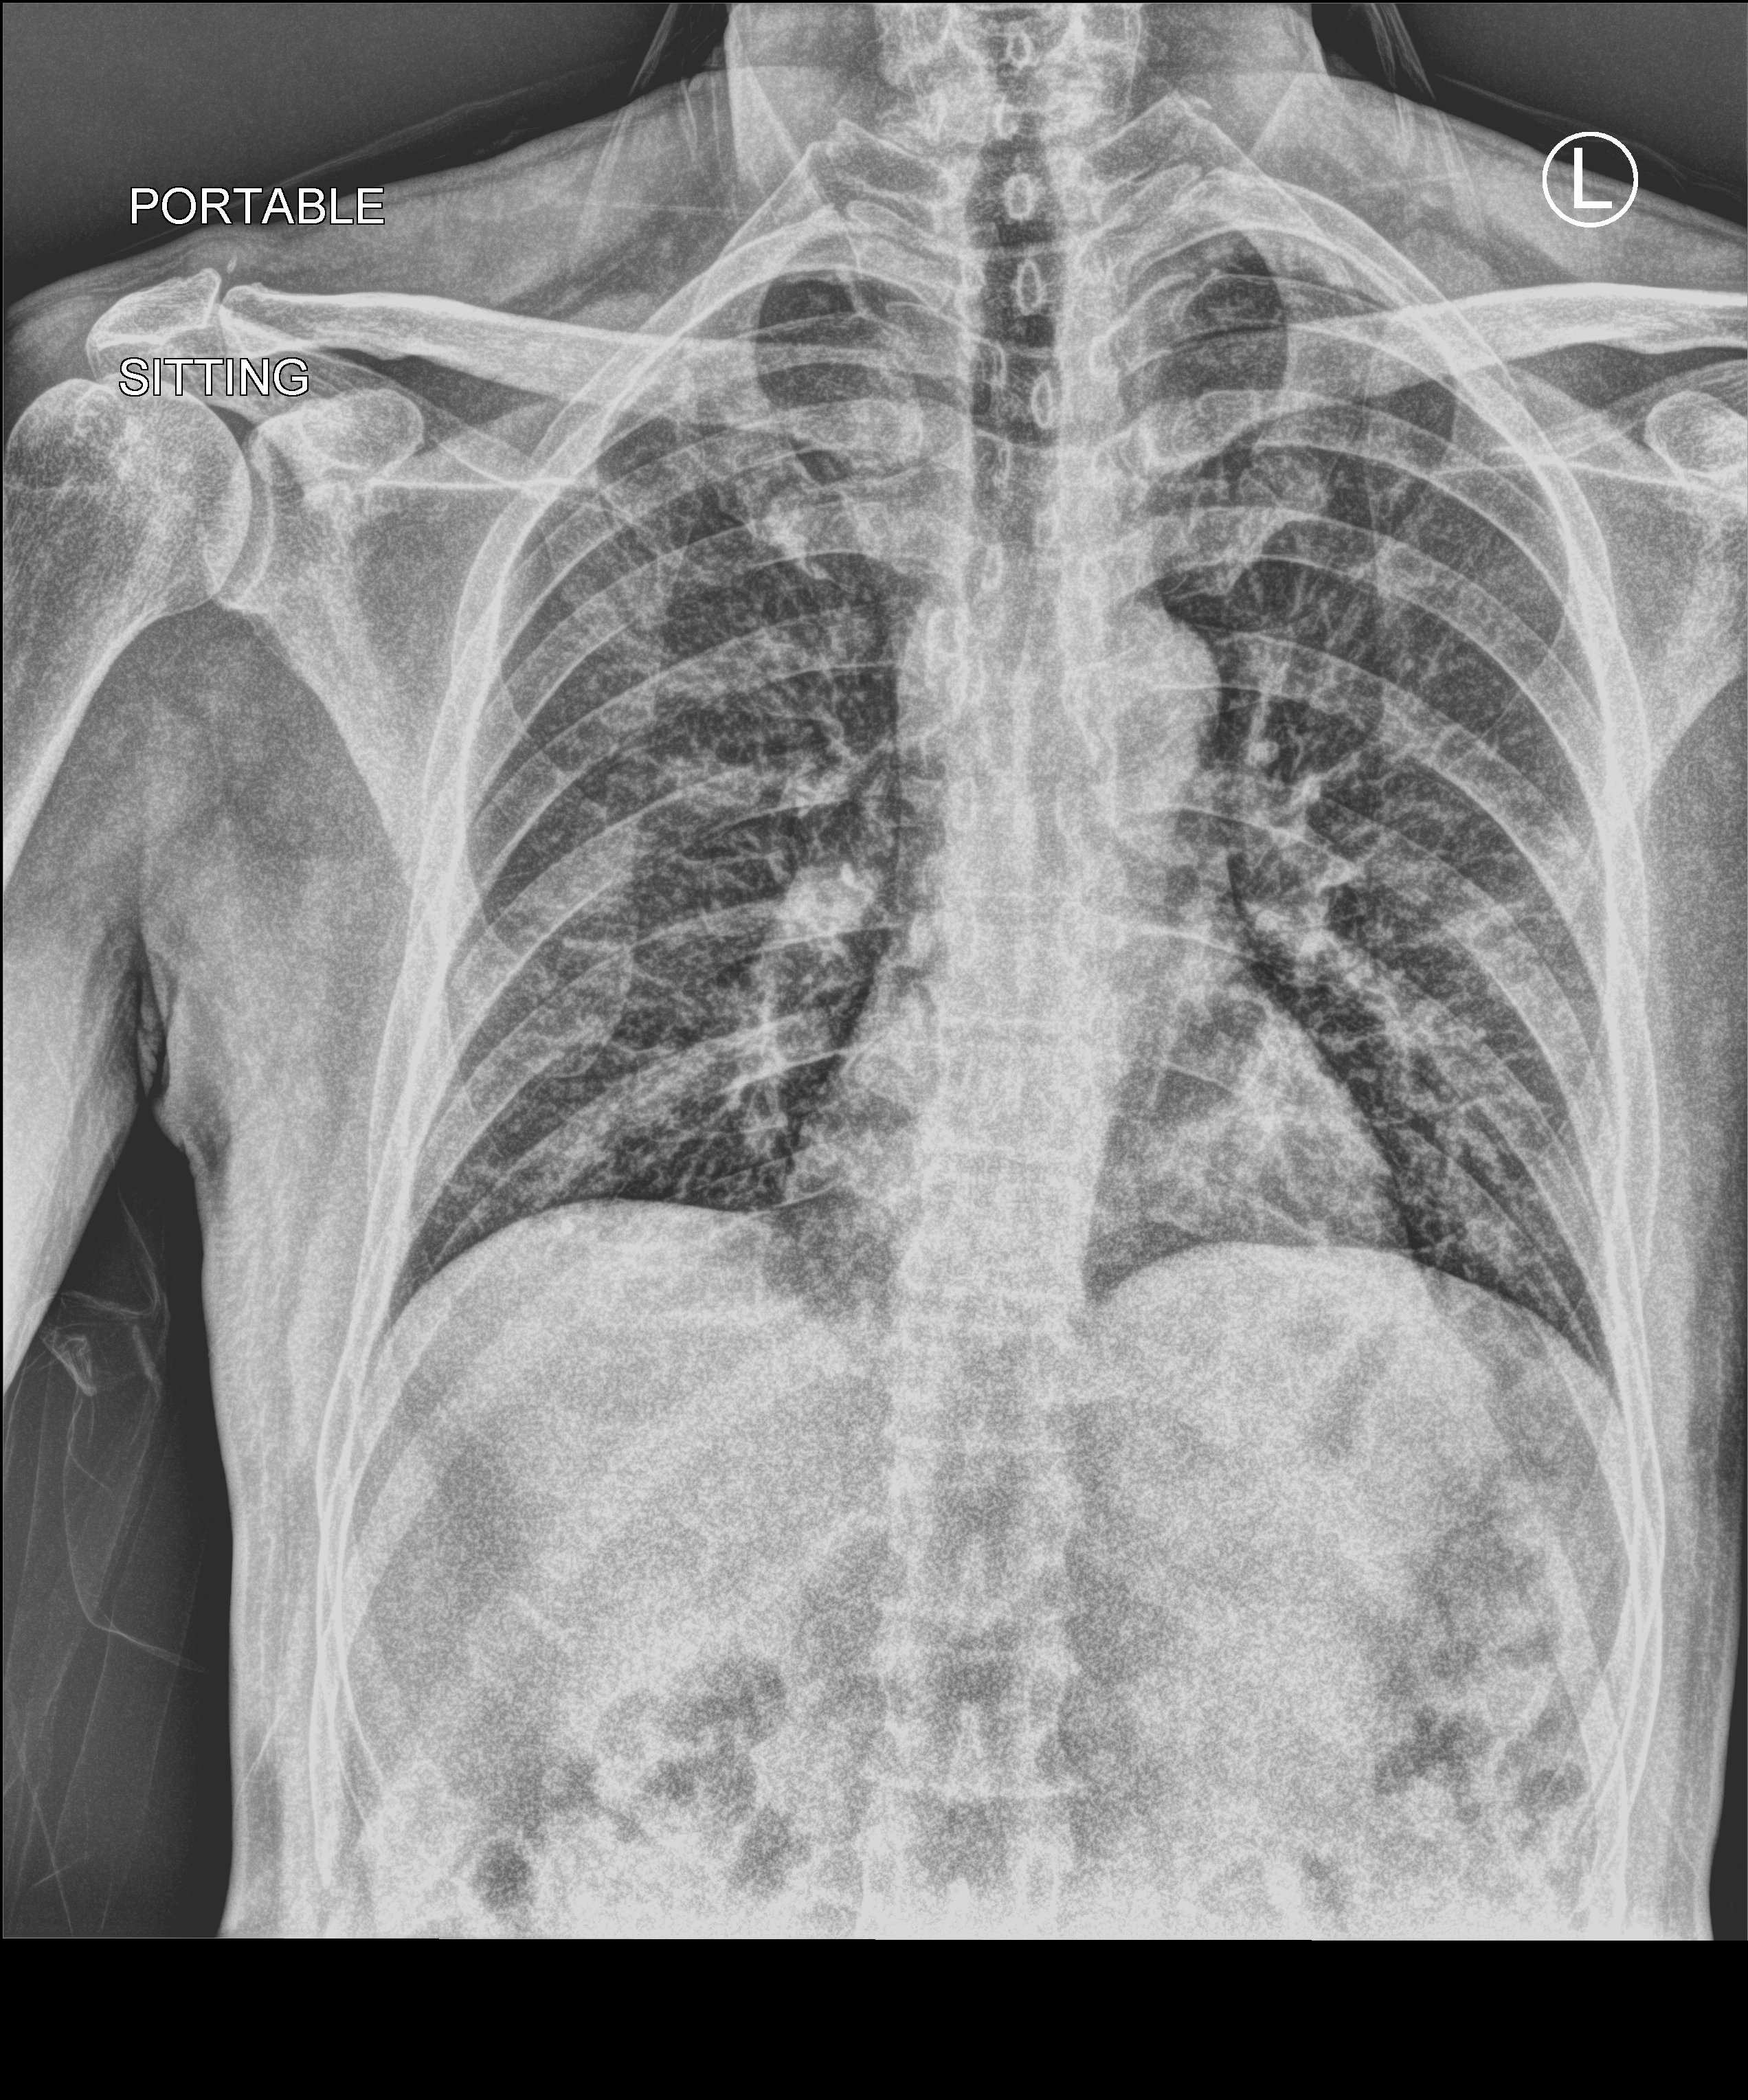
Chest X-ray (portable). Patient hospitalised with COVID-19; male, aged 60–74 years.
Admission-level facts for this patient (not findings on this image; timing relative to this image not recorded): other chronic lung disease (admission record): no; mechanically ventilated during this hospital stay: no.